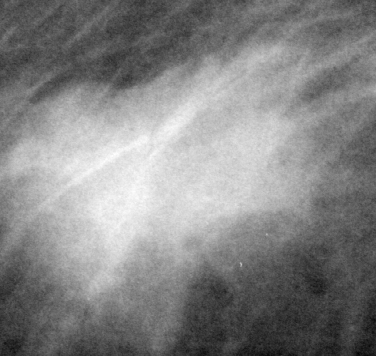
Crop from a digitized film mammogram around one marked abnormality; right breast; MLO view; BI-RADS breast density category 2 (scale 1–4).
Marked abnormality: mass, shape irregular, margins spiculated; BI-RADS assessment category 5; pathology (as recorded): malignant.